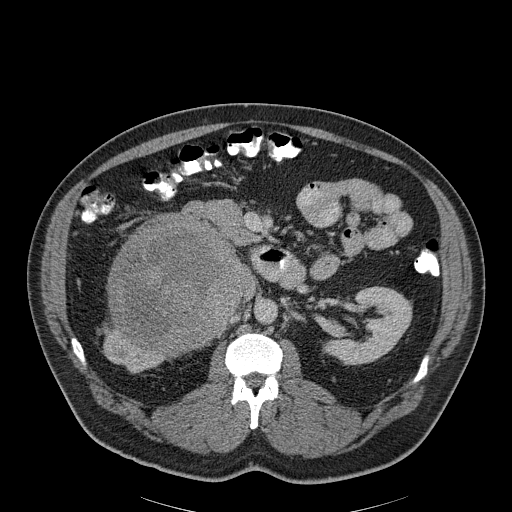
Contrast-enhanced abdominal CT, one axial slice; reconstruction kernel B30f; soft-tissue window (W 400 / L 40 HU); 3 mm slice thickness; 512 × 512 image matrix. Patient: male, 56 years. From the clinical record (not read from this slice): diagnosis: adrenocortical carcinoma; tumour side: right adrenal; tumour size at pathology: 18 cm; Ki-67 index: 2 %; stage (as recorded): 3.
Outlined on this slice (semi-automatic segmentation, software-assisted and operator-edited):
- mass: bounding box <108,215,240,354> (left, top, right, bottom; pixels)